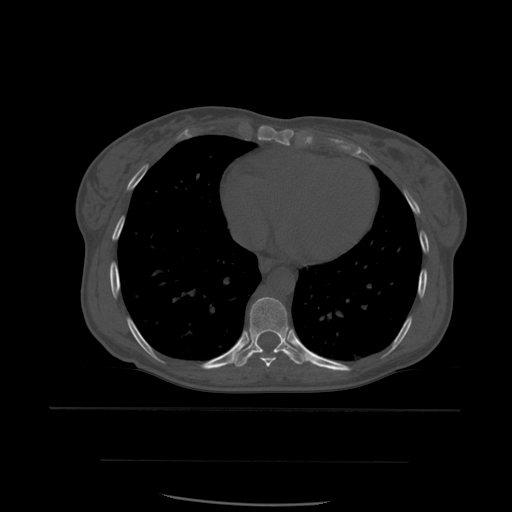
CT including the spine, one axial slice. Slice 343 of 574 in the series (ordered by position). Bone window (W 1800 / L 400 HU). 512 × 512 image matrix, field of view 392 × 392 mm. Patient age 48 years. Case-level facts recorded for this patient, not image findings: primary cancer: lung.
Structures marked on this image (semi-automatically segmented with operator editing):
- T8 vertebra: bounding box [x1, y1, x2, y2] px = [260, 351, 278, 368]
- T9 vertebra: [232, 297, 311, 368]